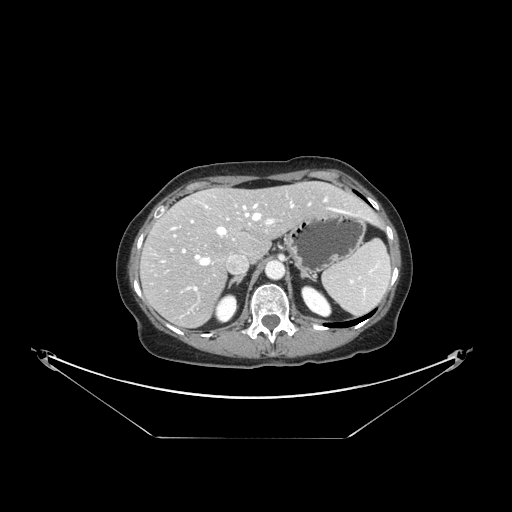
Contrast-enhanced abdominal CT, one axial slice. Slice 104 of 148 in the series (ordered by position). Intravenous contrast given. Soft-tissue window (W 400 / L 40 HU). 2.5 mm slice thickness. 512 × 512 image matrix, field of view 500 × 500 mm. Female patient, age 73 years. From the clinical record (not read from this slice): diagnosis: colorectal cancer liver metastases, imaged before liver resection; multiple liver metastases: no; largest metastasis: 1 cm; disease in both lobes: no.
Annotated regions visible in this slice (outlined manually by an expert reader):
- hepatic veins: bounding box [x1, y1, x2, y2] px = [162, 197, 360, 265]
- liver: [142, 183, 376, 327]
- planned liver remnant (the part of the liver to remain after resection): [168, 183, 375, 259]
- portal vein (with intrahepatic branches): [171, 218, 274, 291]